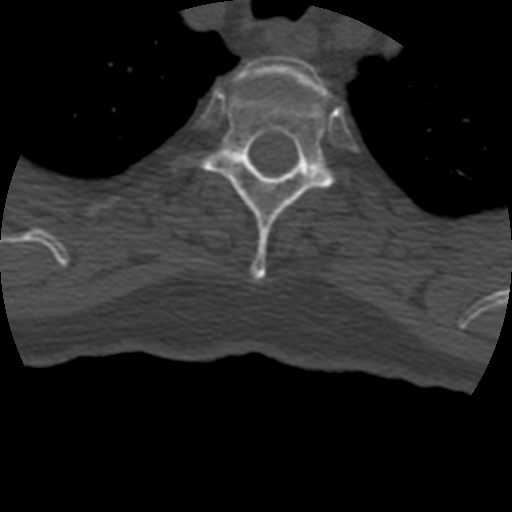
CT including the spine, one axial slice. Bone window (W 1800 / L 400 HU). 512 × 512 image matrix, field of view 160 × 160 mm. Patient age 69 years. Case-level facts recorded for this patient, not image findings: primary cancer: prostate.
Annotated regions visible in this slice (semi-automatically segmented with operator editing):
- T2 vertebra: bounding box (x1, y1, x2, y2) in pixels: (237, 56, 326, 94)
- T3 vertebra: (175, 88, 333, 282)